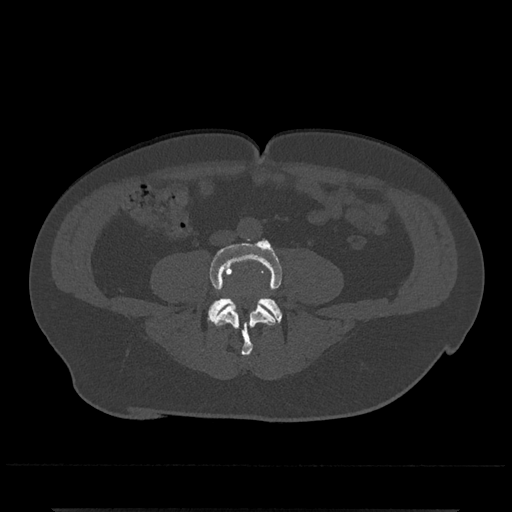
CT including the spine, one axial slice. Slice 129 of 797 in the series (ordered by position). 120 kVp. Bone window (W 1800 / L 400 HU). 512 × 512 image matrix, field of view 393 × 393 mm. Patient: male, 67 years. Case-level facts recorded for this patient, not image findings: primary cancer: prostate.
Structures marked on this image (semi-automatically segmented with operator editing):
- L4 vertebra: bounding box (x1, y1, x2, y2) in pixels: (209, 239, 283, 356)
- L5 vertebra: (208, 297, 282, 322)